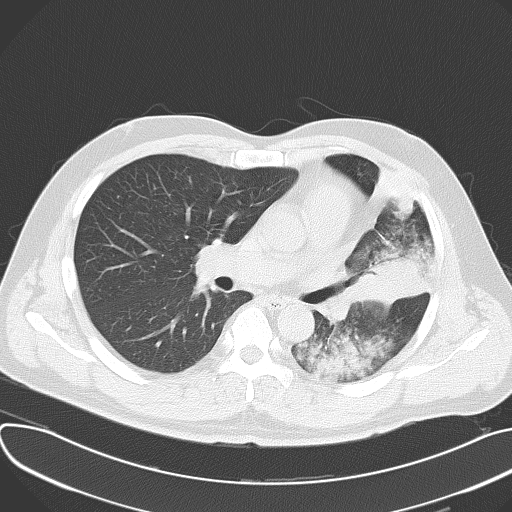
Chest CT, one axial slice. Position 36 of 62 along the scan axis. Reconstruction kernel B70f. 120 kVp. Lung window (W 1500 / L -600 HU). 5 mm slice thickness. 512 × 512 image matrix, field of view 377 × 377 mm. Male patient, age 48 years. From the clinical record (not read from this slice): clinical TNM (as recorded): T4 N0 M0.
Outlined on this slice (bounding box drawn by a radiologist):
- lung tumour (recorded histology: adenocarcinoma): box from (x=348, y=258) to (x=429, y=310) px